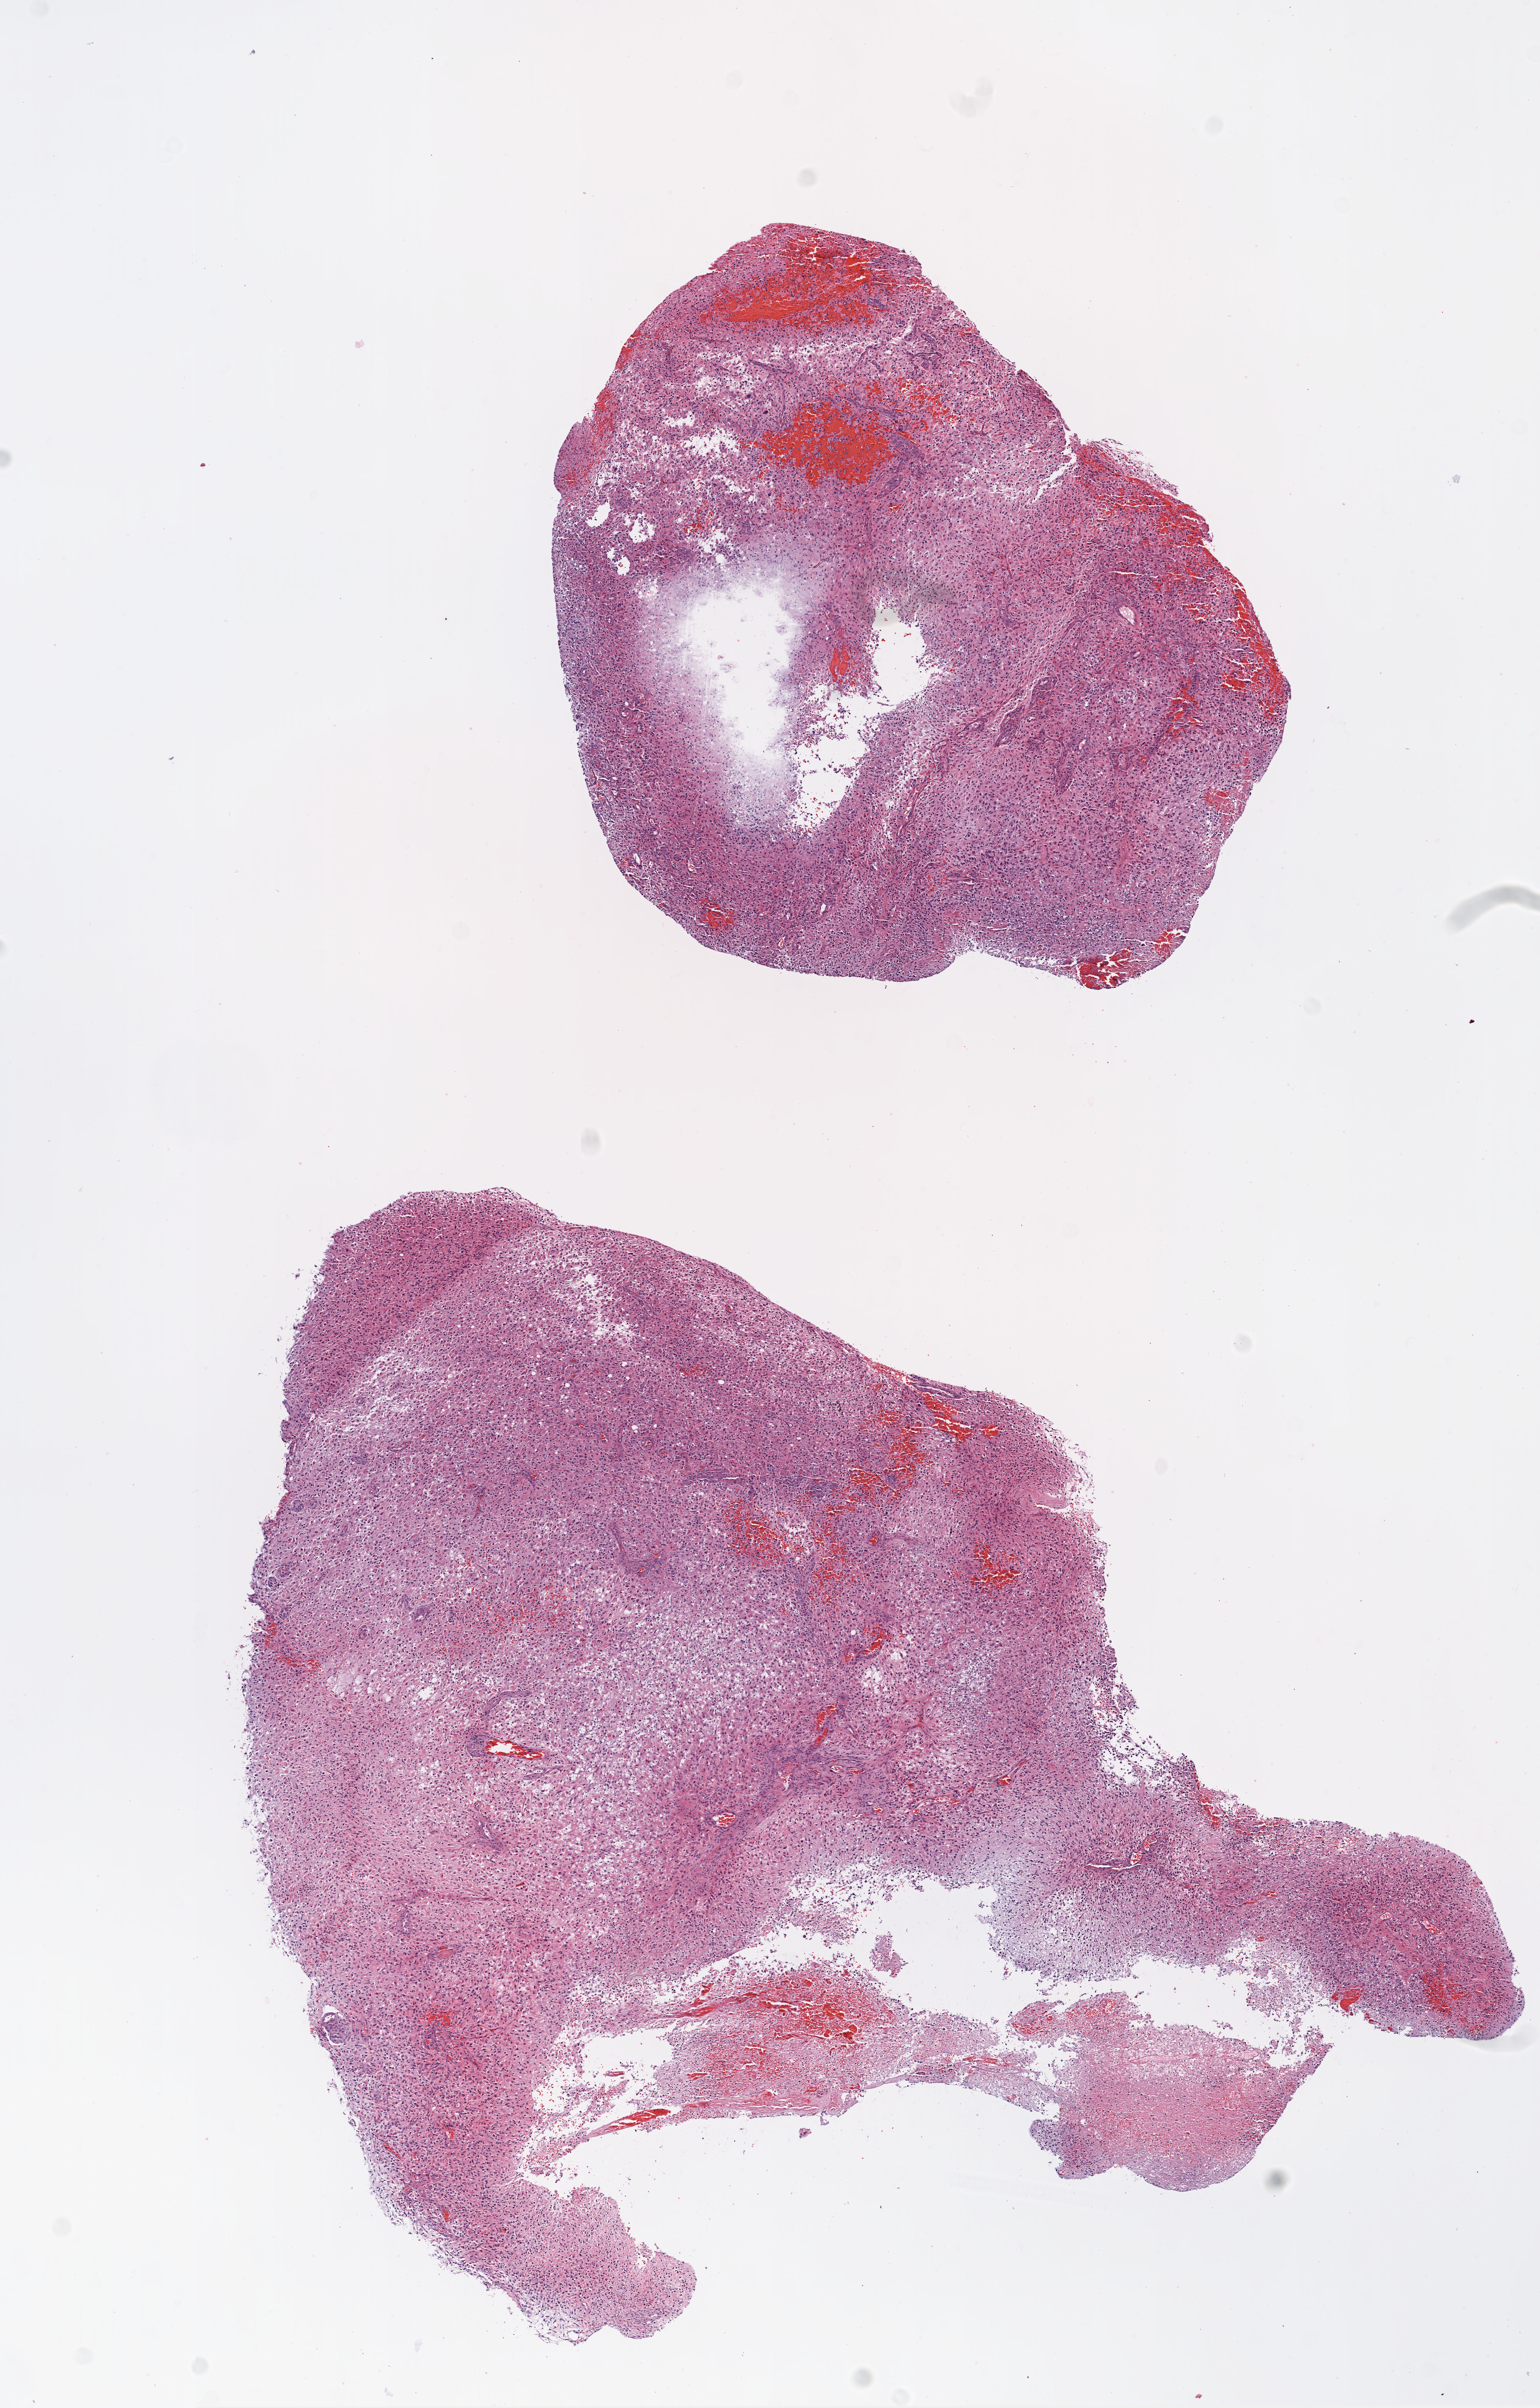
Digitized H&E tissue section (whole slide), low-resolution overview of the scanned area, about 8.0 x 12.5 mm; formalin-fixed paraffin-embedded (FFPE) diagnostic section; sample: primary tumour, brain. Patient: male, age at initial diagnosis 43 years.
* pathologic diagnosis: Glioblastoma